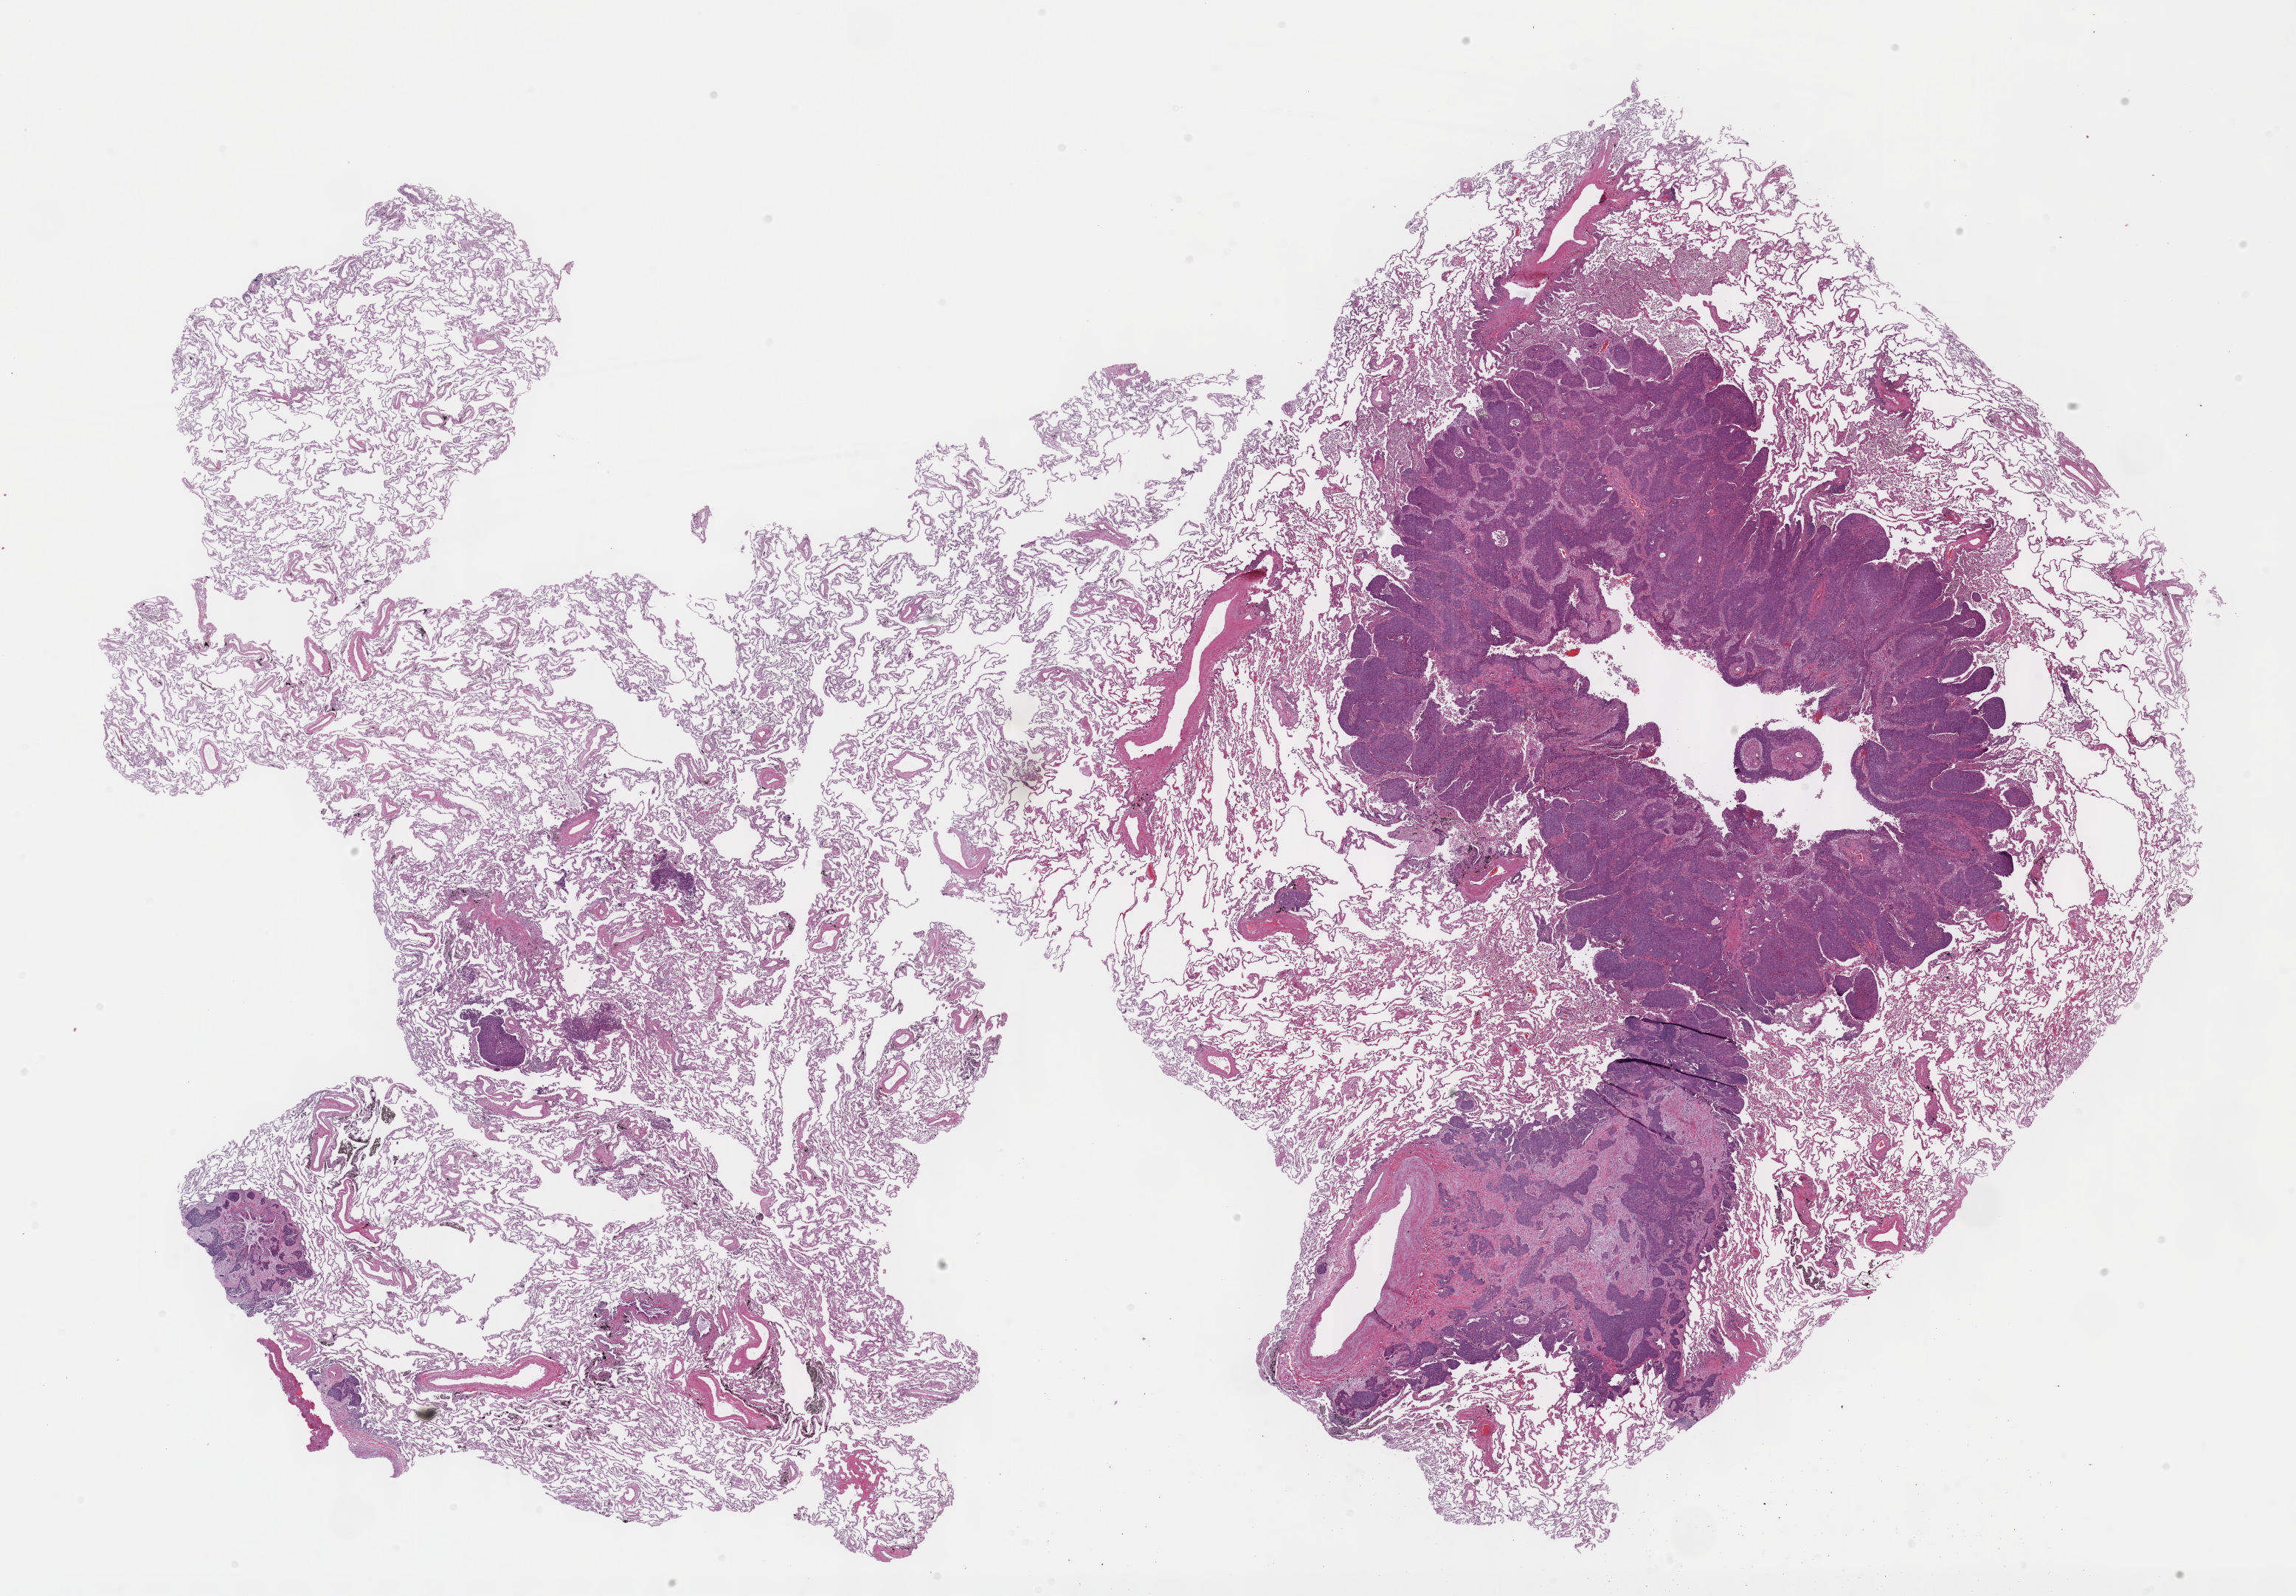
Whole-slide histology image, Hematoxylin and eosin (H&E) stained — whole scanned area (about 25.1 x 17.5 mm) shown as a low-resolution overview. FFPE section. Lung, primary tumour sample. Male patient; age at initial diagnosis 69 years.
TNM: T1 N0 M0. Laterality: right. Pathologic diagnosis: Squamous cell carcinoma, NOS. AJCC pathologic stage: IA.